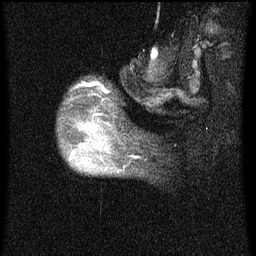
Breast MRI (dynamic contrast-enhanced), one sagittal slice. Slice 15 of 60 in the series (ordered by position). Dynamic contrast-enhanced series, image 2 of 4 at this slice position (ordered by acquisition). 1.5 T. TE 4.2 ms, TR 8 ms. 2 mm slice thickness. 256 × 256 image matrix, field of view 180 × 180 mm. Female patient, age 50 years.
Outlined on this slice (semi-automatic segmentation, software-assisted and operator-edited):
- analysis volume of interest (the breast-tissue region the enhancement analysis was run in; not a lesion): bounding box (x1, y1, x2, y2) in pixels: (63, 84, 124, 175)
- tumour enhancement mask (voxels above the 70 % enhancement threshold inside the analysis volume of interest): (71, 126, 97, 159)